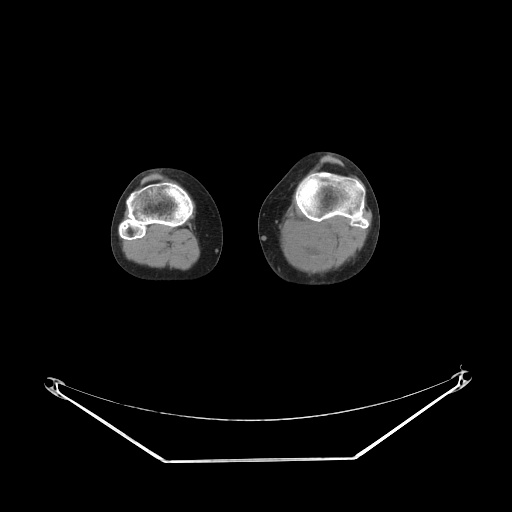
CT of an extremity soft-tissue mass (from a PET/CT study), one axial slice; position 160 of 223 along the scan axis; soft-tissue window (W 400 / L 40 HU); 3.75 mm slice thickness; 512 × 512 image matrix. Female patient. From the clinical record (not read from this slice): histological type: extraskeletal high grade osteogenic sarcoma; grade: high; site of the primary tumour: left calf.
Outlined on this slice (expert contour drawn on MRI and transferred to this co-registered scan by the dataset authors):
- gross tumour volume (mass): box from (x=283, y=226) to (x=330, y=263) px